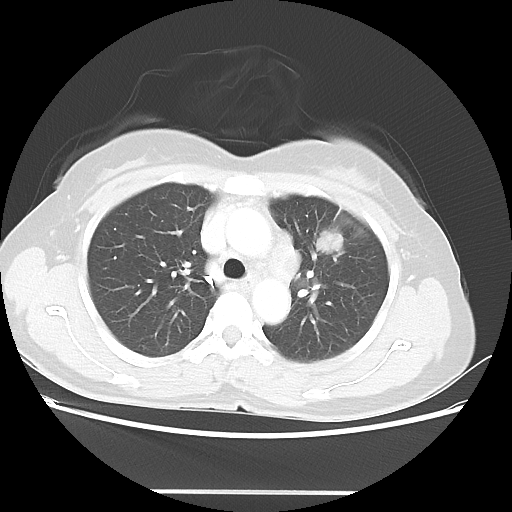
Chest CT, one axial slice; position 32 of 46 along the scan axis; reconstruction kernel LUNG; 100 kVp; lung window (W 1500 / L -600 HU); 512 × 512 image matrix, field of view 360 × 360 mm. Patient: female, 50 years. Case-level facts recorded for this patient, not image findings: clinical TNM (as recorded): T1c N1 M0; histopathological grade: G3.
Structures marked on this image (bounding box drawn by a radiologist):
- lung tumour (recorded histology: adenocarcinoma): bounding box <313,226,346,257> (left, top, right, bottom; pixels)